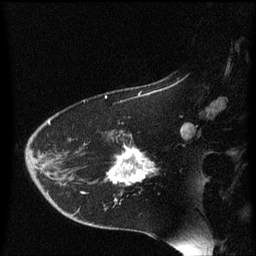
Breast MRI (dynamic contrast-enhanced), one sagittal slice; position 41 of 60 along the scan axis; dynamic contrast-enhanced series, image 2 of 3 at this slice position (ordered by acquisition); 1.5 T; TE 4.2 ms, TR 8.4 ms; 2 mm slice thickness; 256 × 256 image matrix. Patient: female, 54 years. Case-level facts recorded for this patient, not image findings: setting: breast cancer imaged before/during neoadjuvant chemotherapy; receptor status: HR-positive, HER2-negative.
Annotated regions visible in this slice (semi-automatically segmented with operator editing):
- analysis volume of interest (the breast-tissue region the enhancement analysis was run in; not a lesion): bounding box (x1, y1, x2, y2) in pixels: (109, 130, 155, 187)
- tumour enhancement mask (voxels above the 70 % enhancement threshold inside the analysis volume of interest): (111, 148, 155, 185)